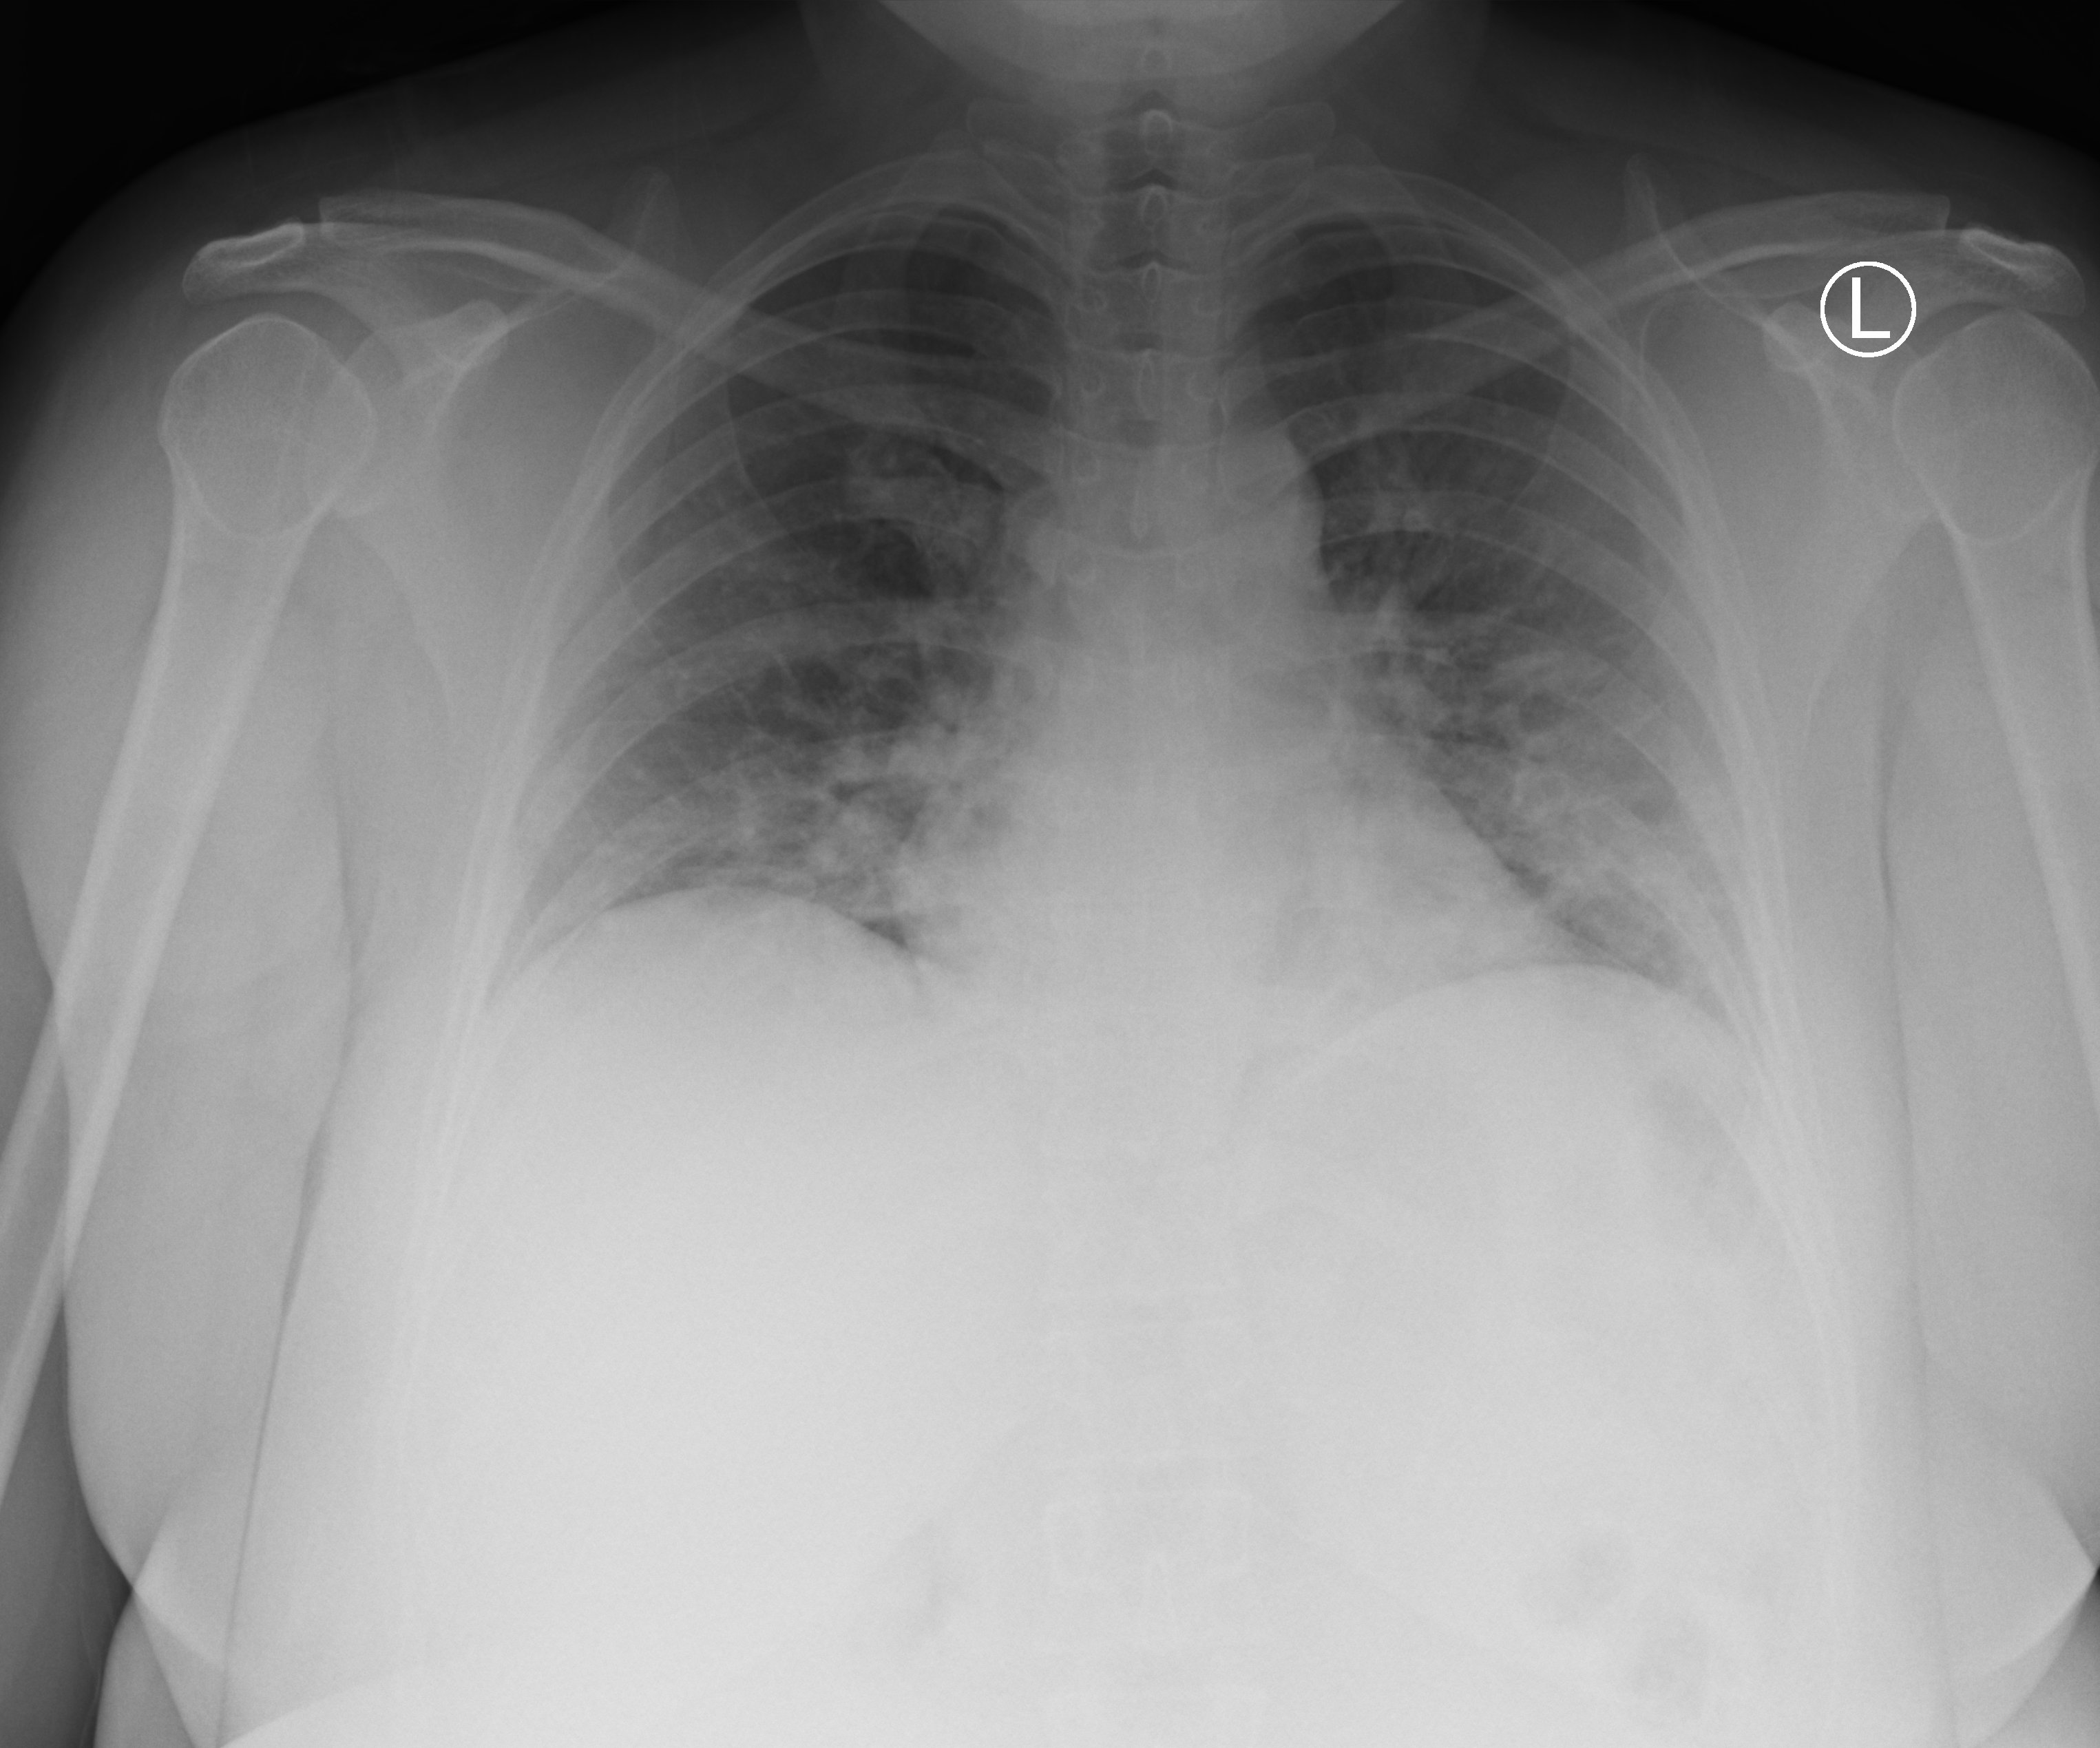
Chest X-ray (portable), anteroposterior (AP) projection. Female patient hospitalised with COVID-19, age 18–59 years.
From the hospital-stay record, not from the radiograph (when in the stay this image was taken is not recorded): length of hospital stay: 16 days; chronic kidney disease (admission record): no; hypertension (admission record): no.